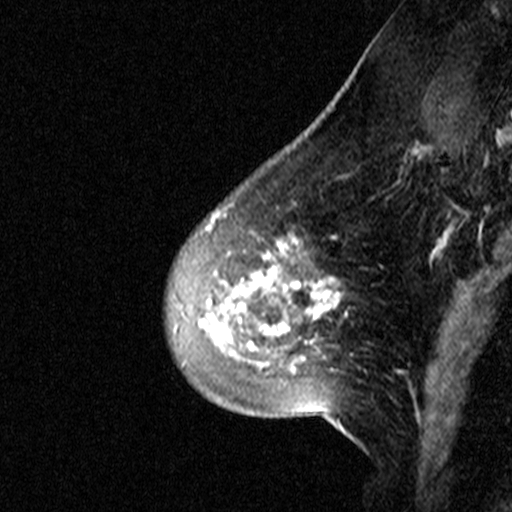
Breast MRI (dynamic contrast-enhanced), one sagittal slice. Dynamic contrast-enhanced study with each time point stored as its own series, time point 2 of 3 at this slice position (early post-contrast, ordered by acquisition time). 1.5 T. TE 4.5 ms, TR 11 ms. 3 mm slice thickness. 512 × 512 image matrix, field of view 200 × 200 mm. Patient: female, 46 years. Case-level facts recorded for this patient, not image findings: setting: breast cancer imaged before/during neoadjuvant chemotherapy; receptor status: HER2-positive.
Annotated regions visible in this slice (semi-automatically segmented with operator editing):
- analysis volume of interest (the breast-tissue region the enhancement analysis was run in; not a lesion): bounding box (x1, y1, x2, y2) in pixels: (165, 172, 359, 393)
- tumour enhancement mask (voxels above the 90 % enhancement threshold inside the analysis volume of interest): (208, 213, 340, 360)